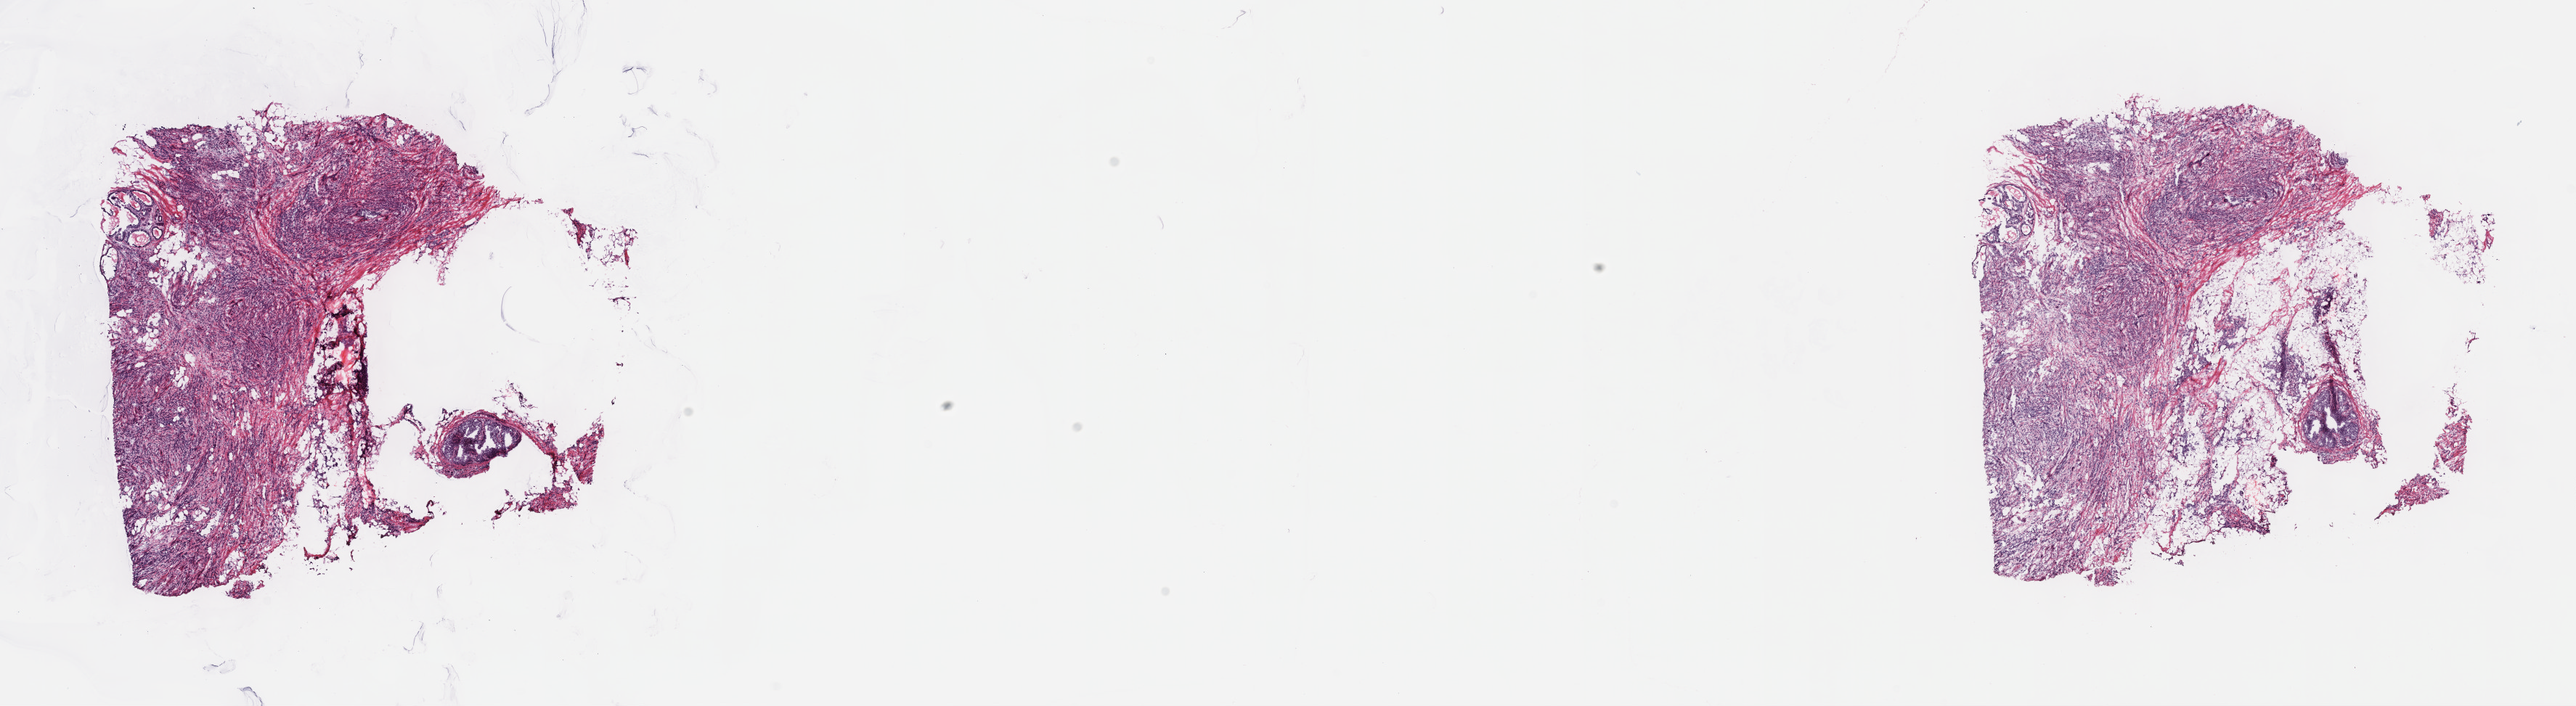
H&E whole-slide image, low-resolution overview of the scanned area, about 28.7 x 7.9 mm (slide scanned at 40x); frozen section from the top of the tissue portion; primary tumour sample from the breast. Patient: female, age at initial diagnosis 54 years. Slide review estimates, as recorded: tumour cells 70%, tumour nuclei 80%, normal cells 30%, stromal cells 0%, necrosis 0%. Inflammatory infiltration, as recorded: lymphocyte infiltration 0%, monocyte infiltration 0%, neutrophil infiltration 0%.
* diagnosis: Infiltrating lobular mixed with other types of carcinoma (upper-inner quadrant of breast)
* TNM: T2 N1a M0
* AJCC pathologic stage: IIB (7th edition)
* laterality: right